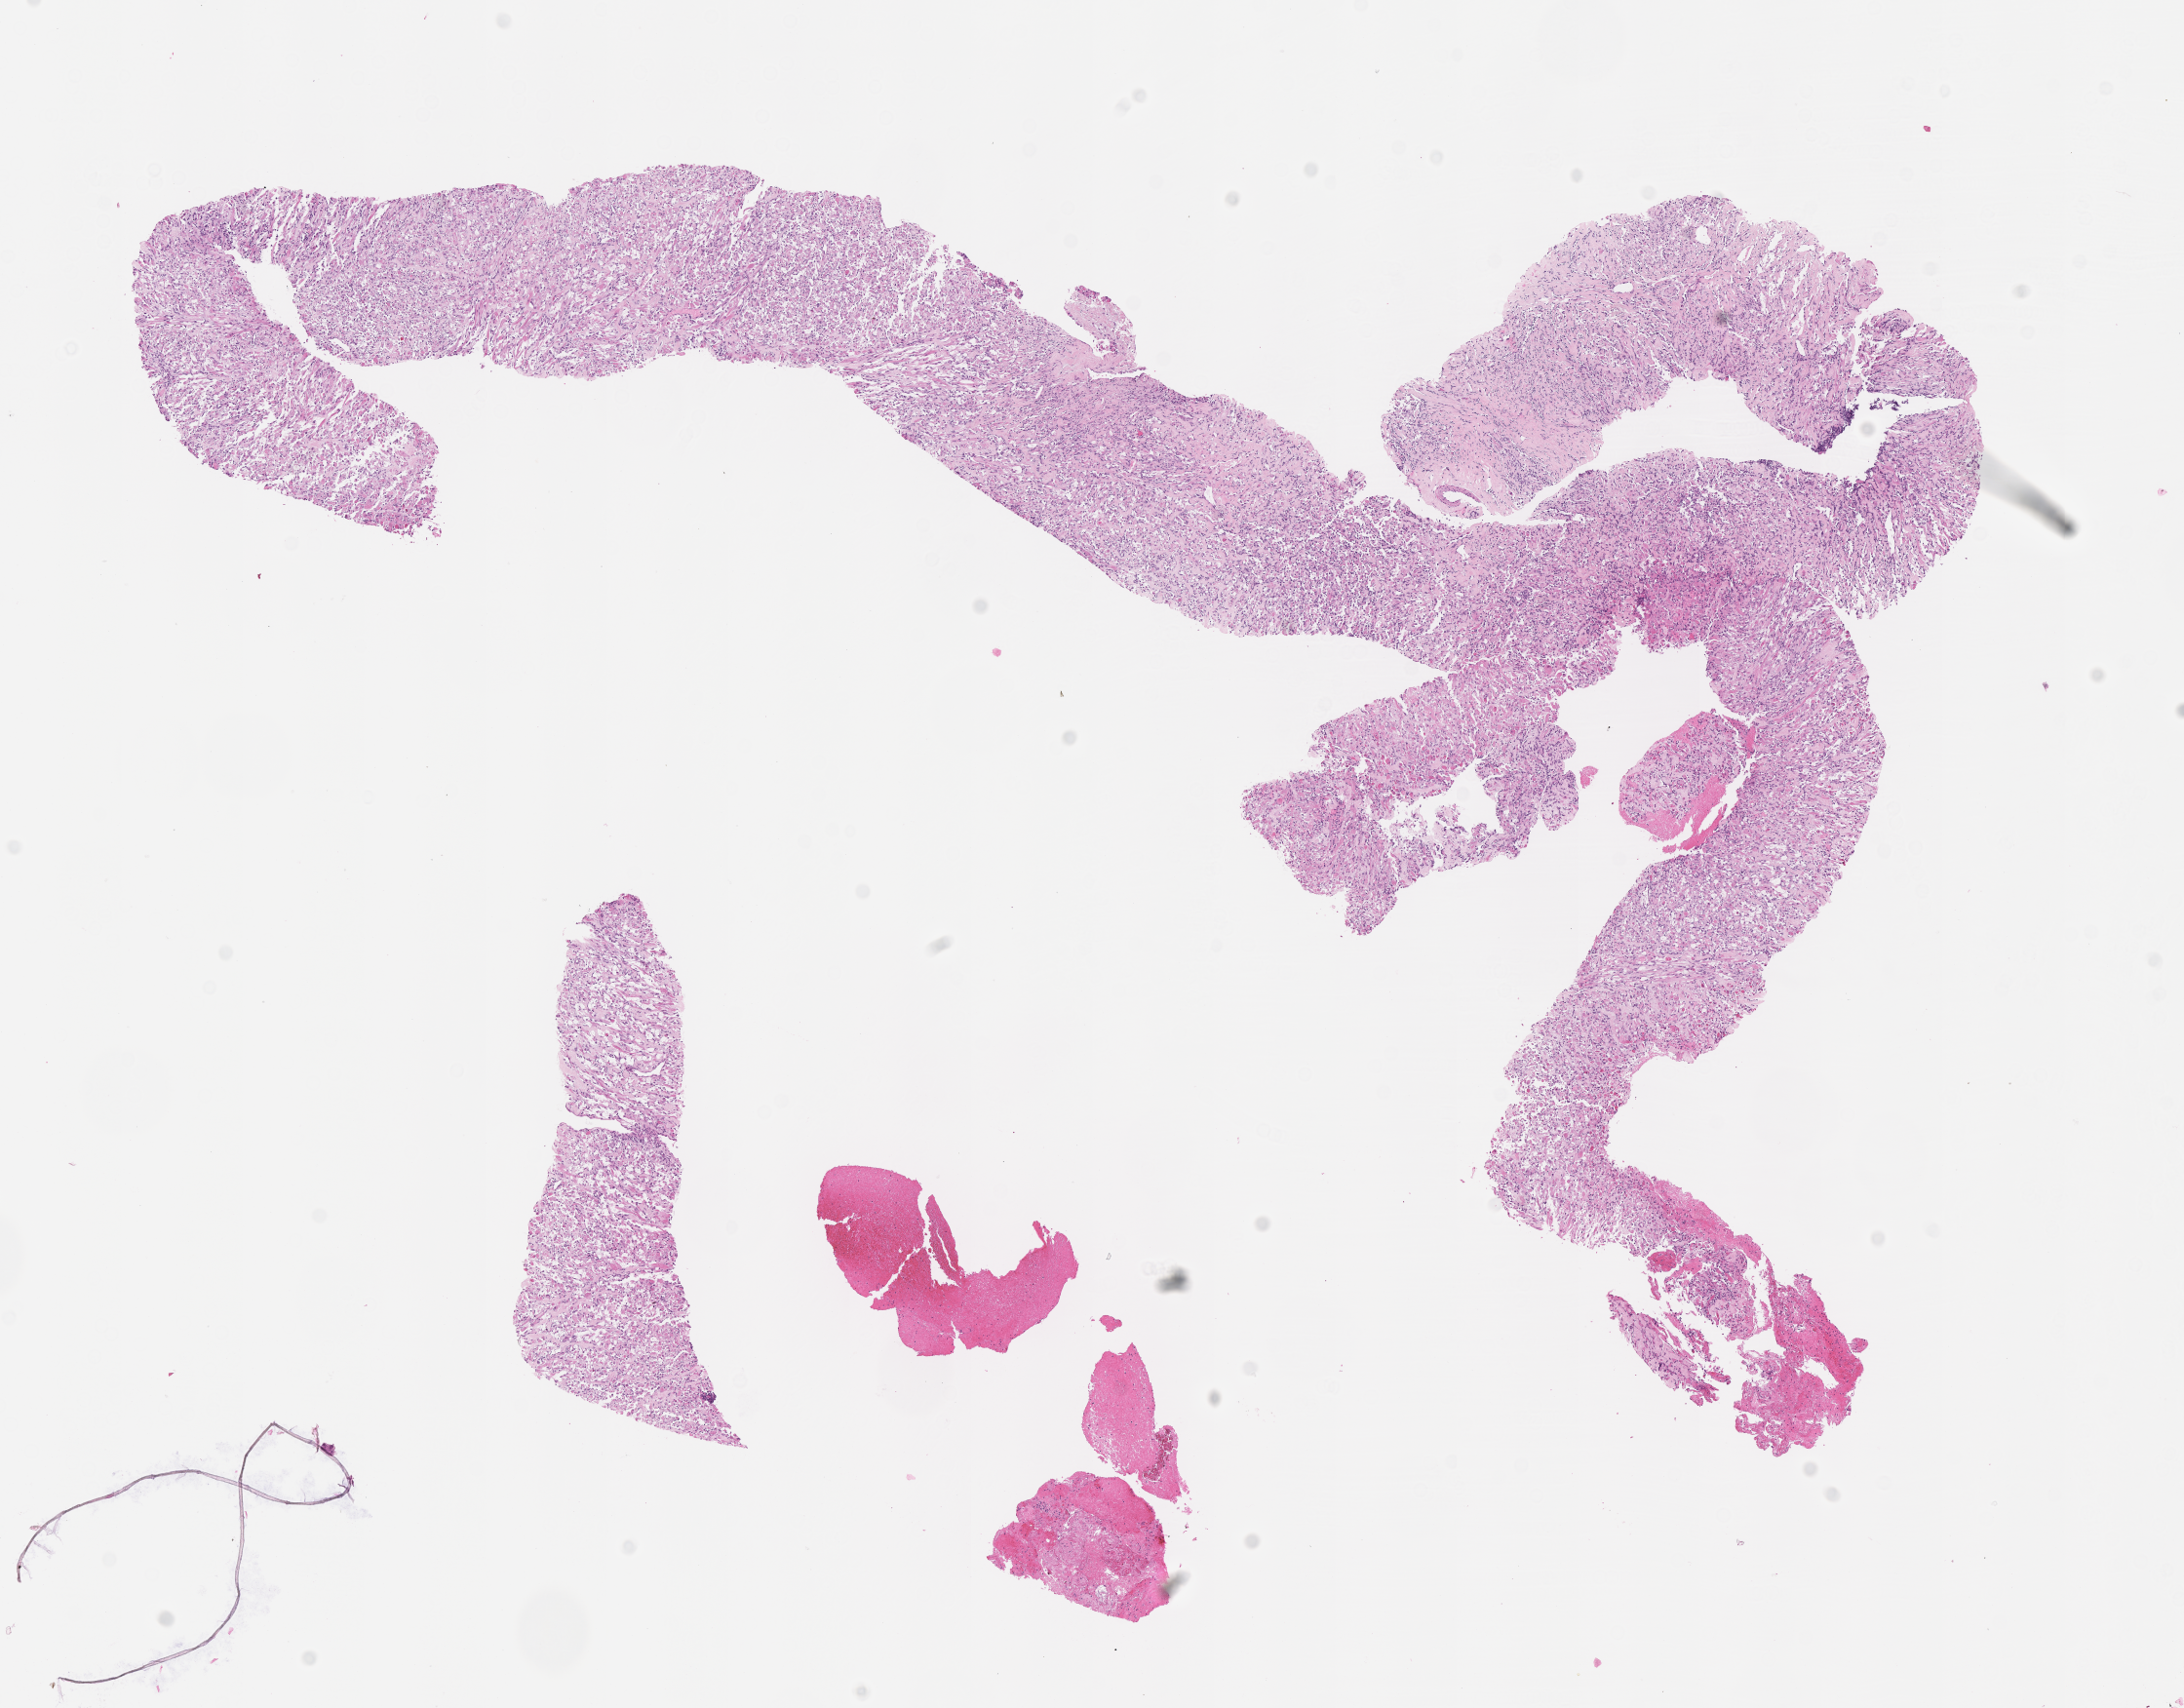
Digitized haematoxylin and eosin-stained section of tumor tissue, shown as a low-resolution overview of the whole scanned area (about 9.1 x 7.1 mm), formalin-fixed paraffin-embedded section, site: soft tissue, ear-left (periauricular). Patient: male, age 8.8 years at diagnosis.
Metastatic status at presentation (as recorded): non-metastatic. Stage (as recorded): 3. Diagnosis: rhabdomyosarcoma; histological classification: embryonal rhabdomyosarcoma. Primary site (case record): infratemporal Fossa.